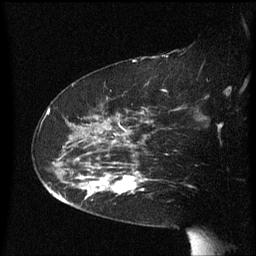
Breast MRI (dynamic contrast-enhanced), one sagittal slice; slice 41 of 60 in the series (ordered by position); dynamic contrast-enhanced series, image 2 of 3 at this slice position (ordered by acquisition); 1.5 T; TE 4.2 ms, TR 8.4 ms; 2.3 mm slice thickness; 256 × 256 image matrix, field of view 200 × 200 mm. Female patient, age 63 years. Case-level facts recorded for this patient, not image findings: setting: breast cancer imaged before/during neoadjuvant chemotherapy; receptor status: HER2-positive.
Annotated regions visible in this slice (semi-automatic segmentation, software-assisted and operator-edited):
- analysis volume of interest (the breast-tissue region the enhancement analysis was run in; not a lesion): bounding box [x1, y1, x2, y2] px = [71, 144, 147, 207]
- tumour enhancement mask (voxels above the 70 % enhancement threshold inside the analysis volume of interest): [76, 176, 143, 197]